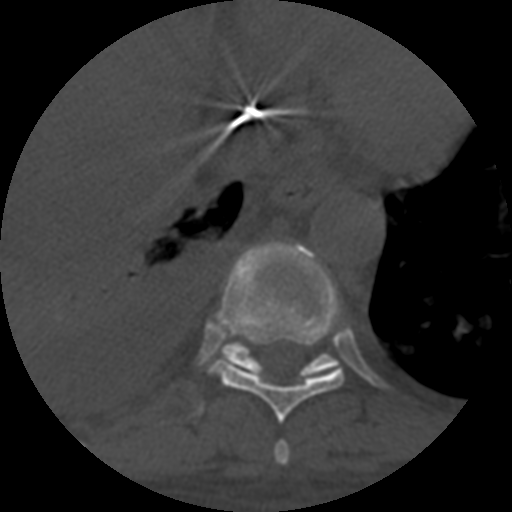
CT including the spine, one axial slice; slice 372 of 708 in the series (ordered by position); 120 kVp; one of 3 acquisitions stored at this slice position; bone window (W 1800 / L 400 HU); 1.25 mm slice thickness; 512 × 512 image matrix. Patient age 55 years. From the clinical record (not read from this slice): primary cancer: colon.
Structures marked on this image (semi-automatic segmentation, software-assisted and operator-edited):
- T10 vertebra: bounding box <221,344,338,380> (left, top, right, bottom; pixels)
- T8 vertebra: <274,441,289,465>
- T9 vertebra: <210,242,345,423>